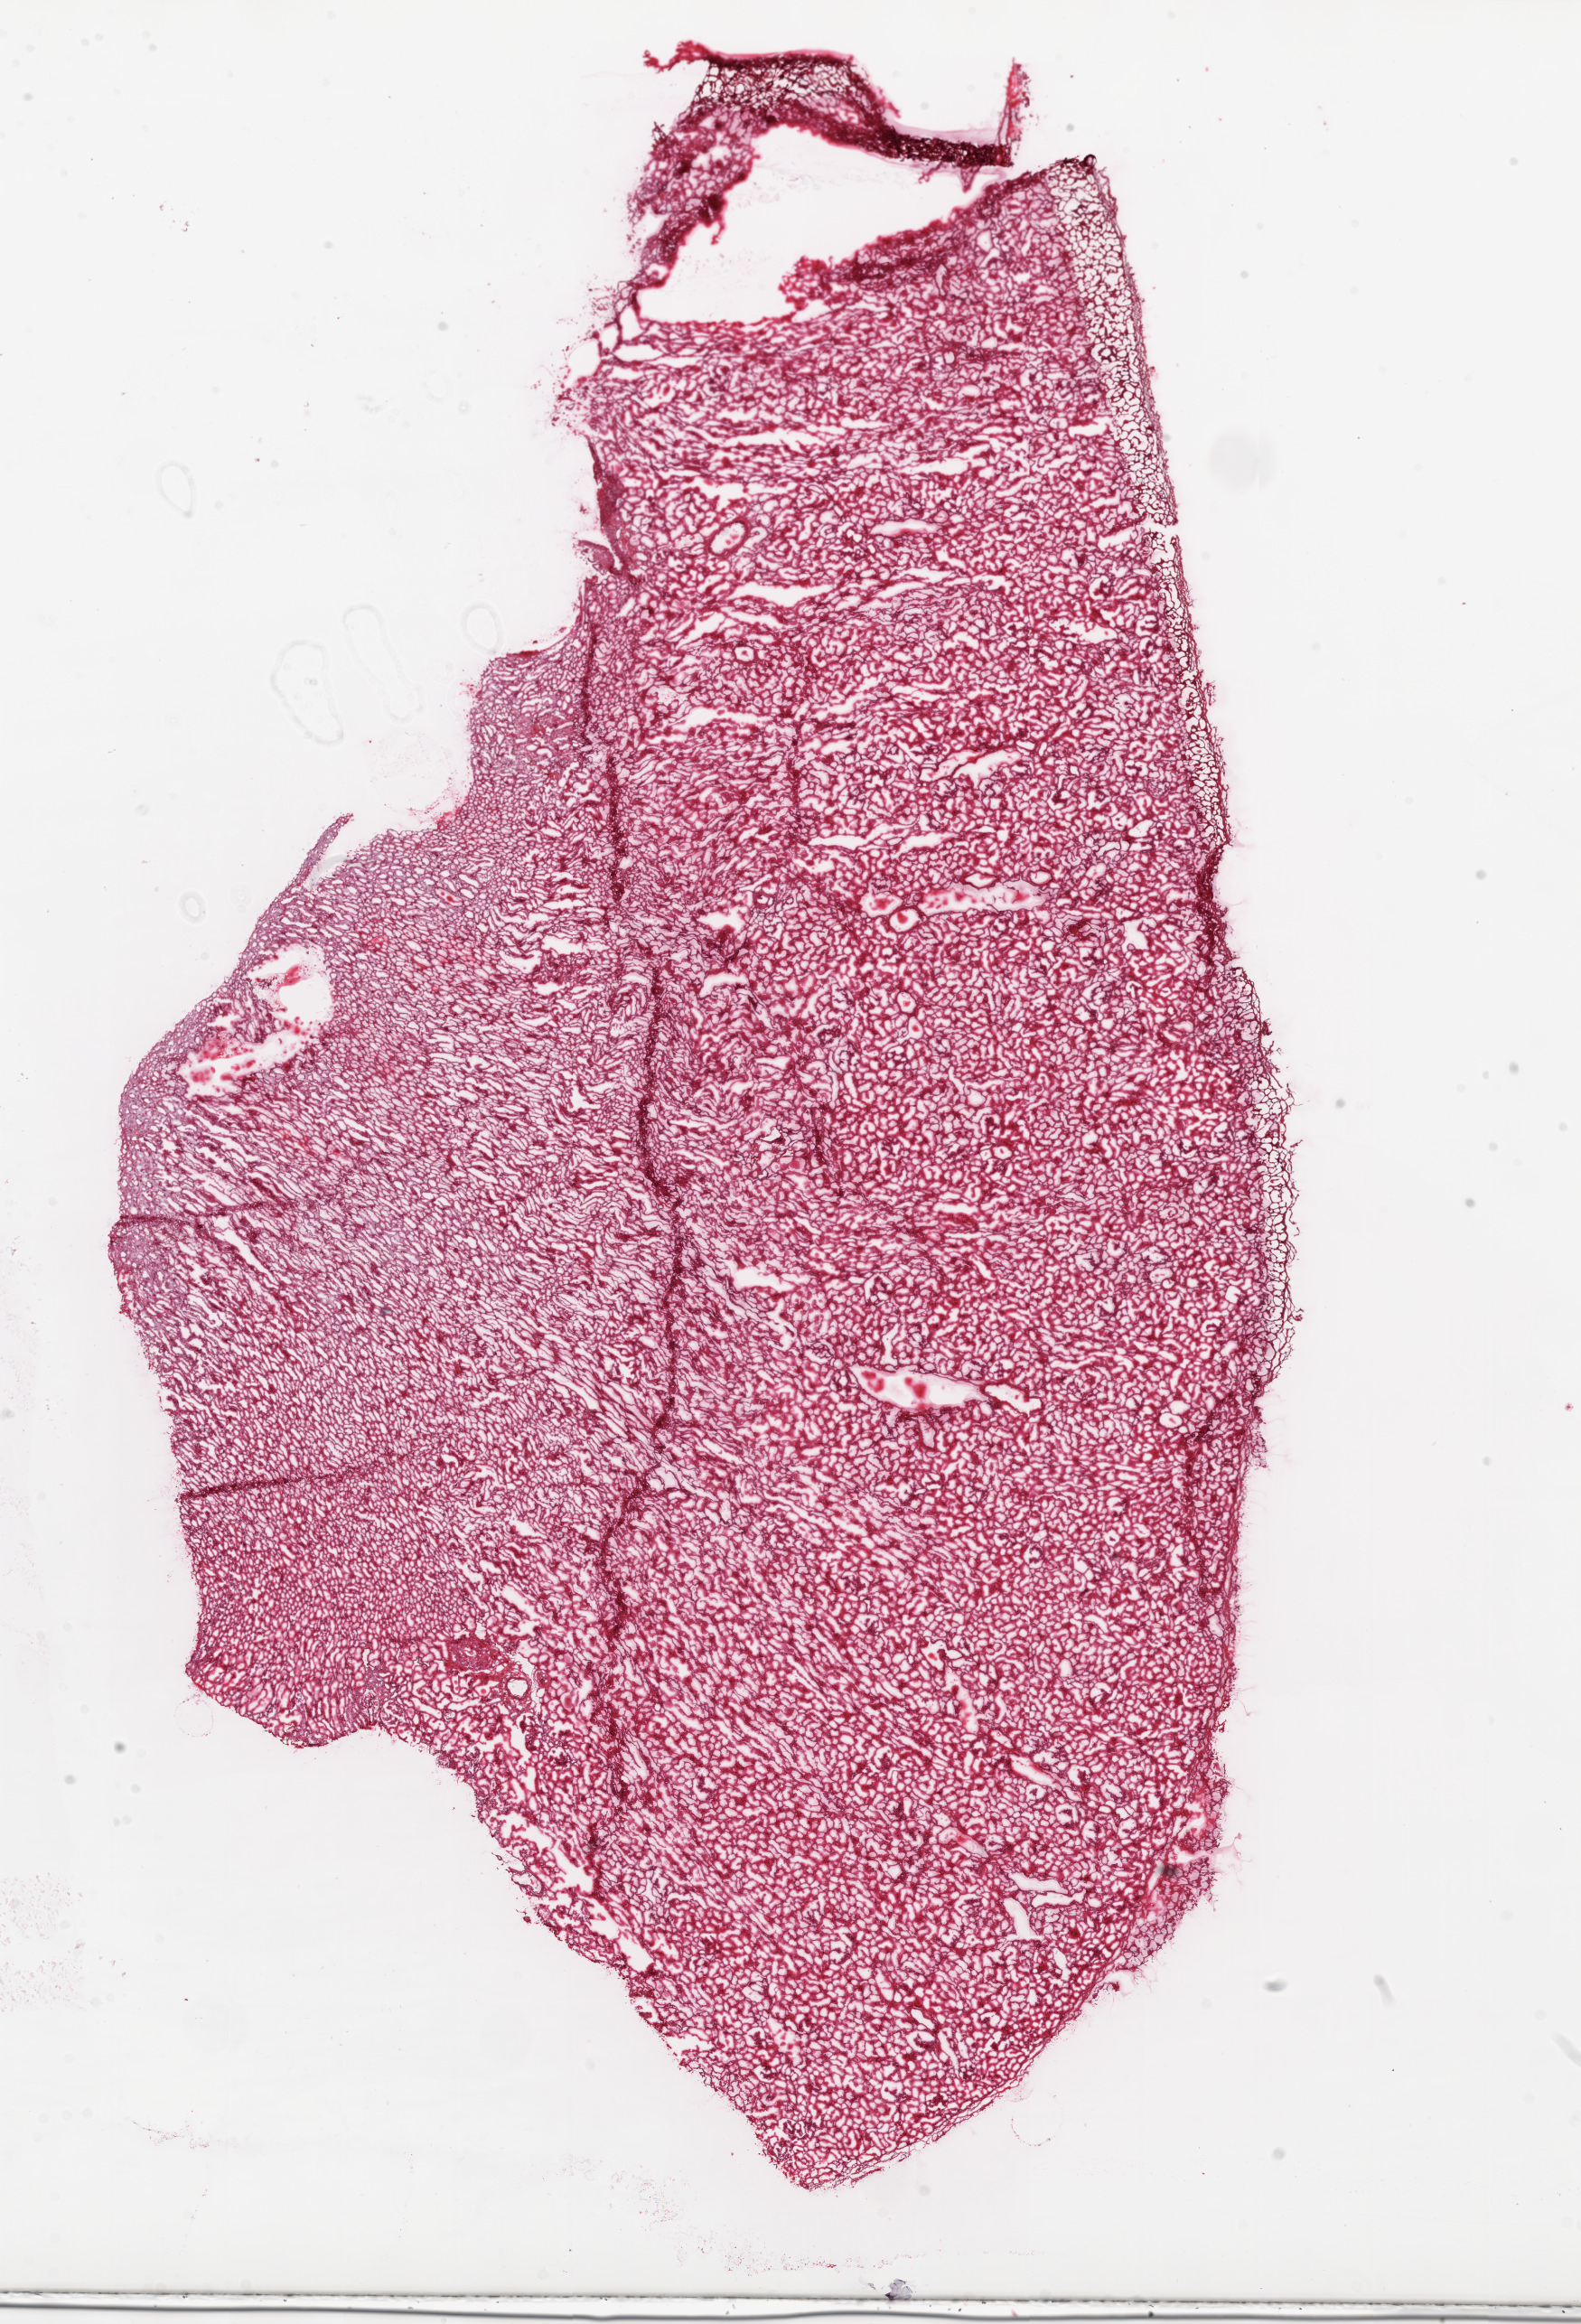
Digitized Hematoxylin and eosin (H&E) stained tissue section (whole slide) — a low-resolution overview of the entire scanned area, about 14.0 x 20.6 mm. Frozen section from the top of the tissue portion. Solid tissue normal (non-tumour tissue) sample from the kidney. Male, age 46 years at initial diagnosis.
This section: solid tissue normal sample (biorepository sample class). Patient diagnosis: Clear cell adenocarcinoma, NOS.